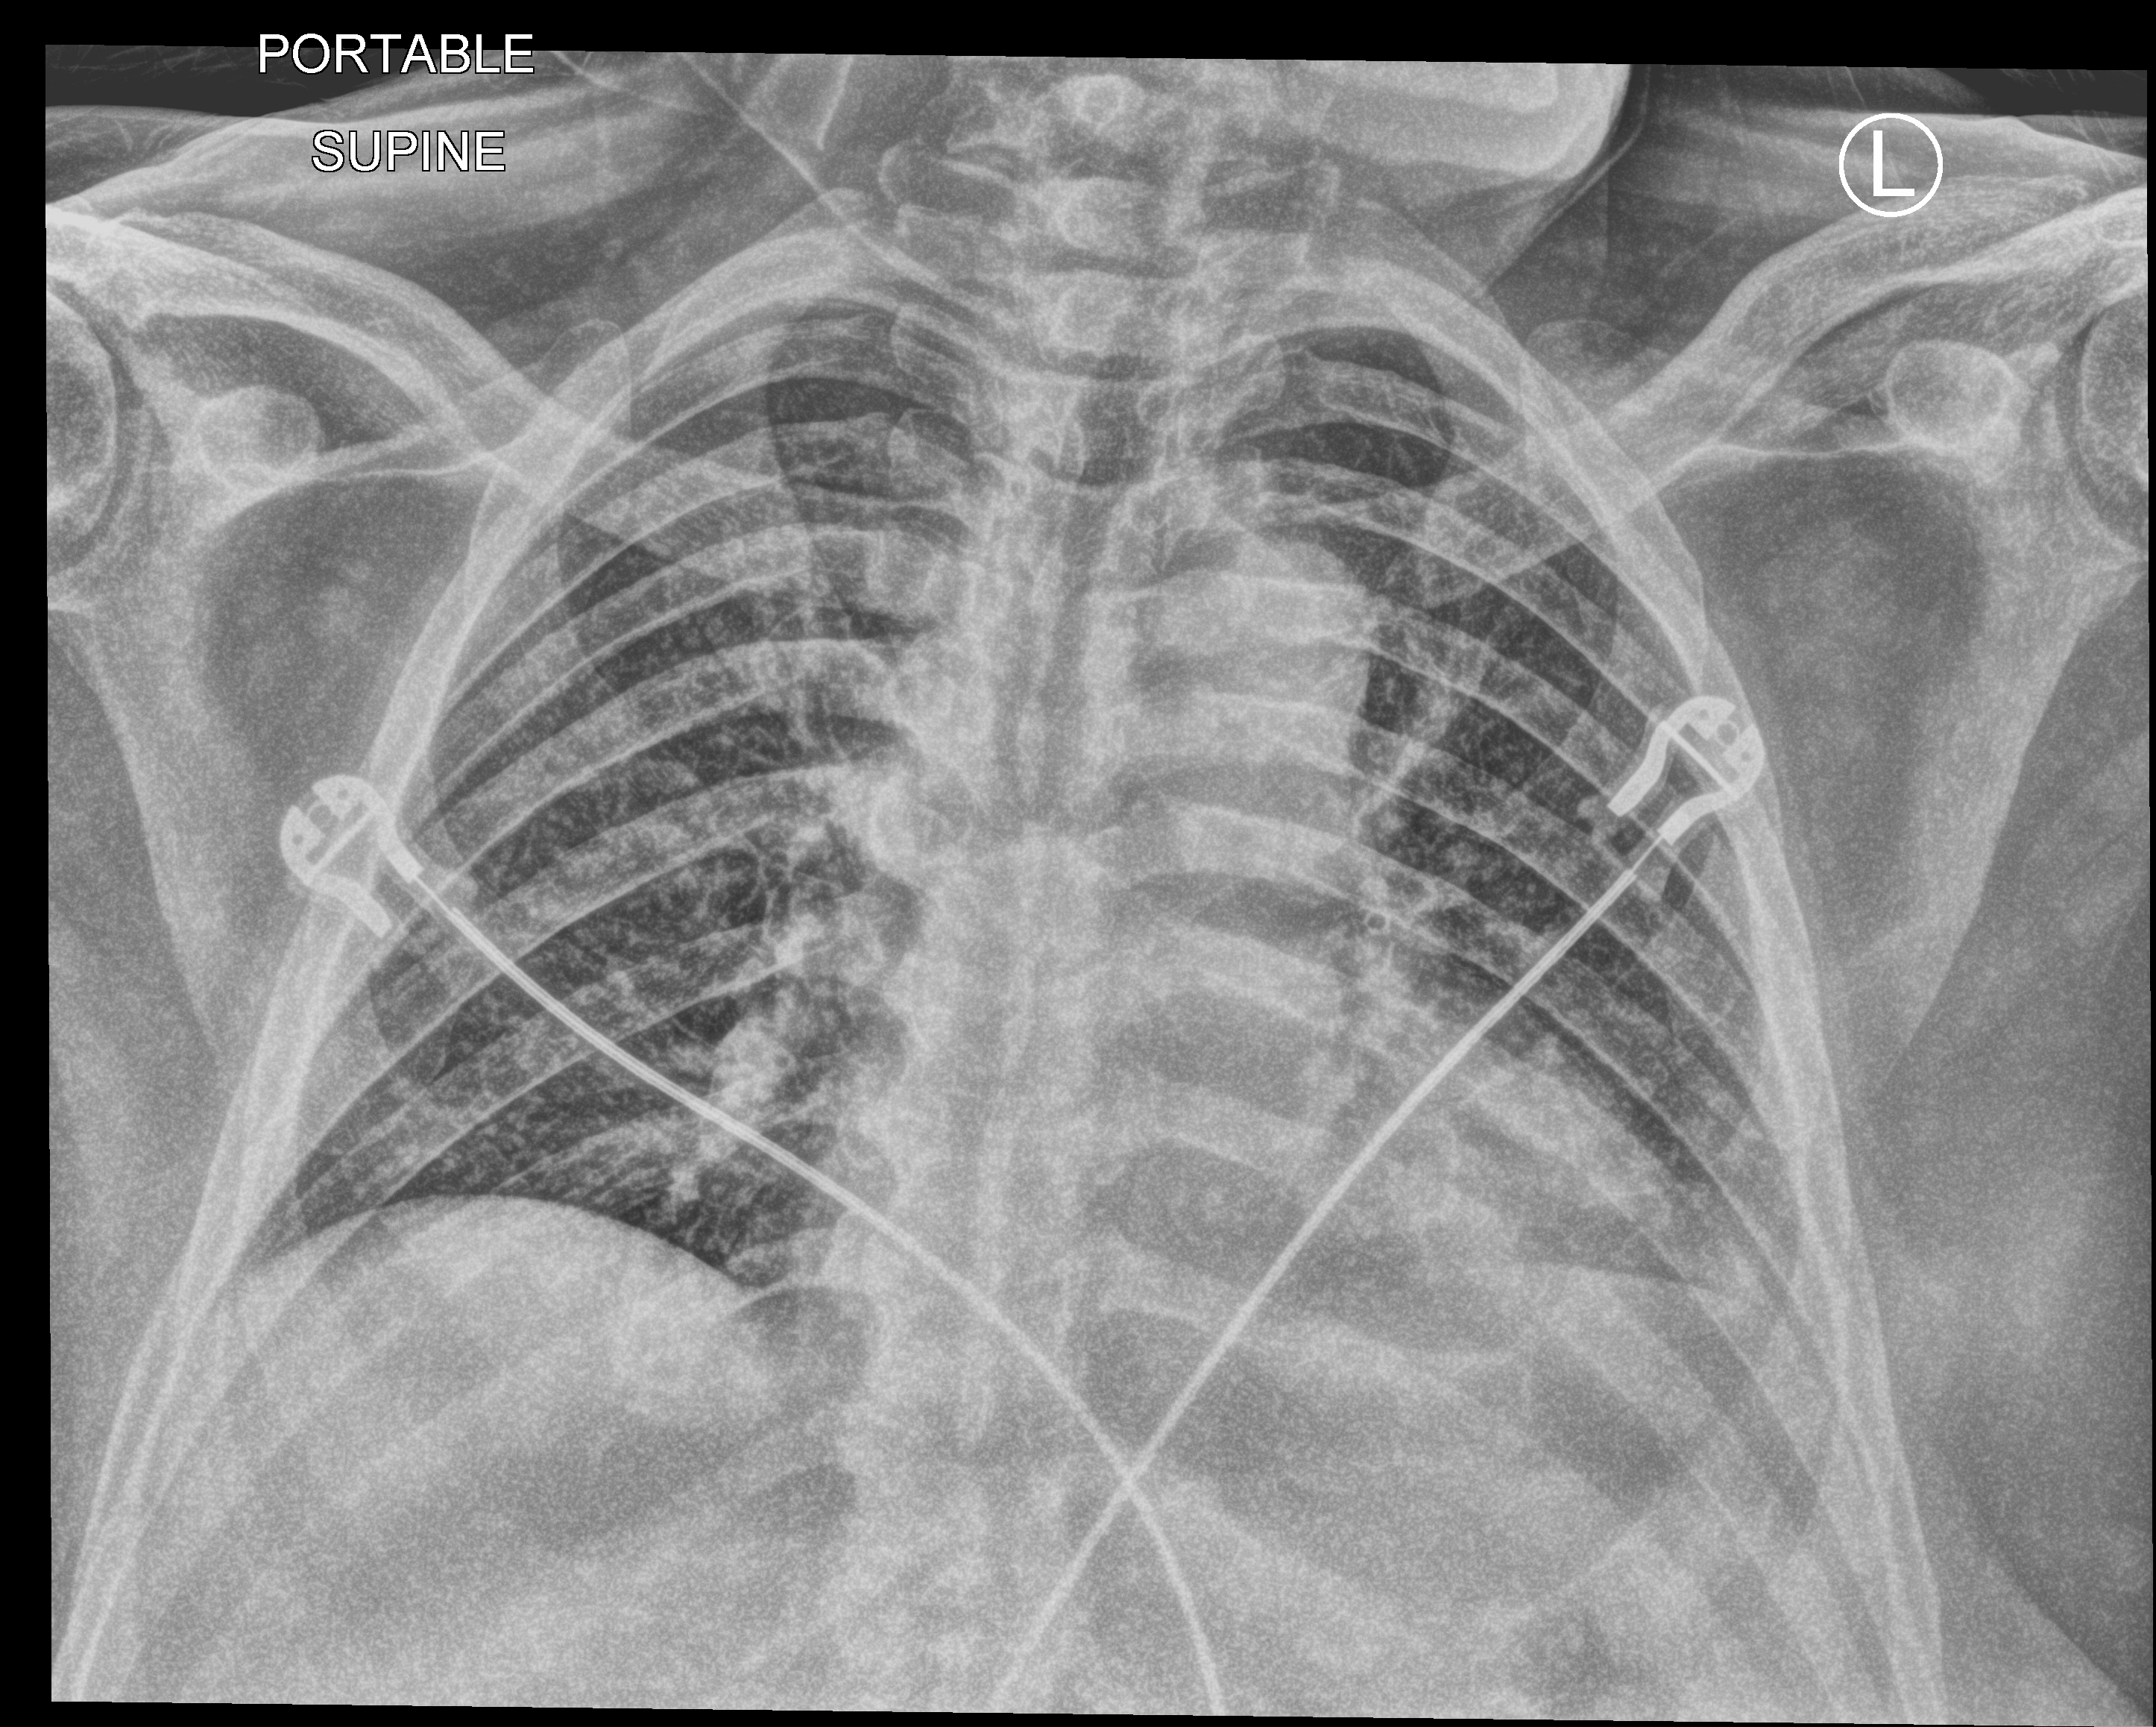
Chest X-ray (portable), anteroposterior (AP) projection. Patient hospitalised with COVID-19; male, aged 75–90 years.
From the hospital-stay record, not from the radiograph (when in the stay this image was taken is not recorded): admitted to intensive care during this hospital stay: yes.